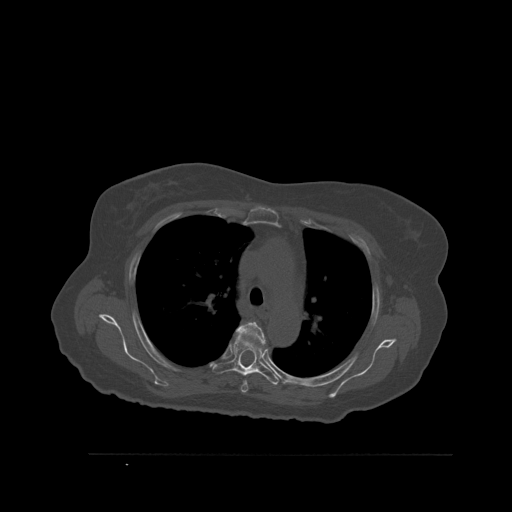
CT including the spine, one axial slice; position 399 of 527 along the scan axis; bone window (W 1800 / L 400 HU); 1.5 mm slice thickness; 512 × 512 image matrix, field of view 470 × 470 mm. Female patient, age 73 years. From the clinical record (not read from this slice): primary cancer: breast; vertebrae with lytic lesions (as recorded): L2.
Outlined on this slice (semi-automatically segmented with operator editing):
- T4 vertebra: box from (x=236, y=321) to (x=267, y=393) px
- T5 vertebra: (x=212, y=334)–(x=279, y=385)